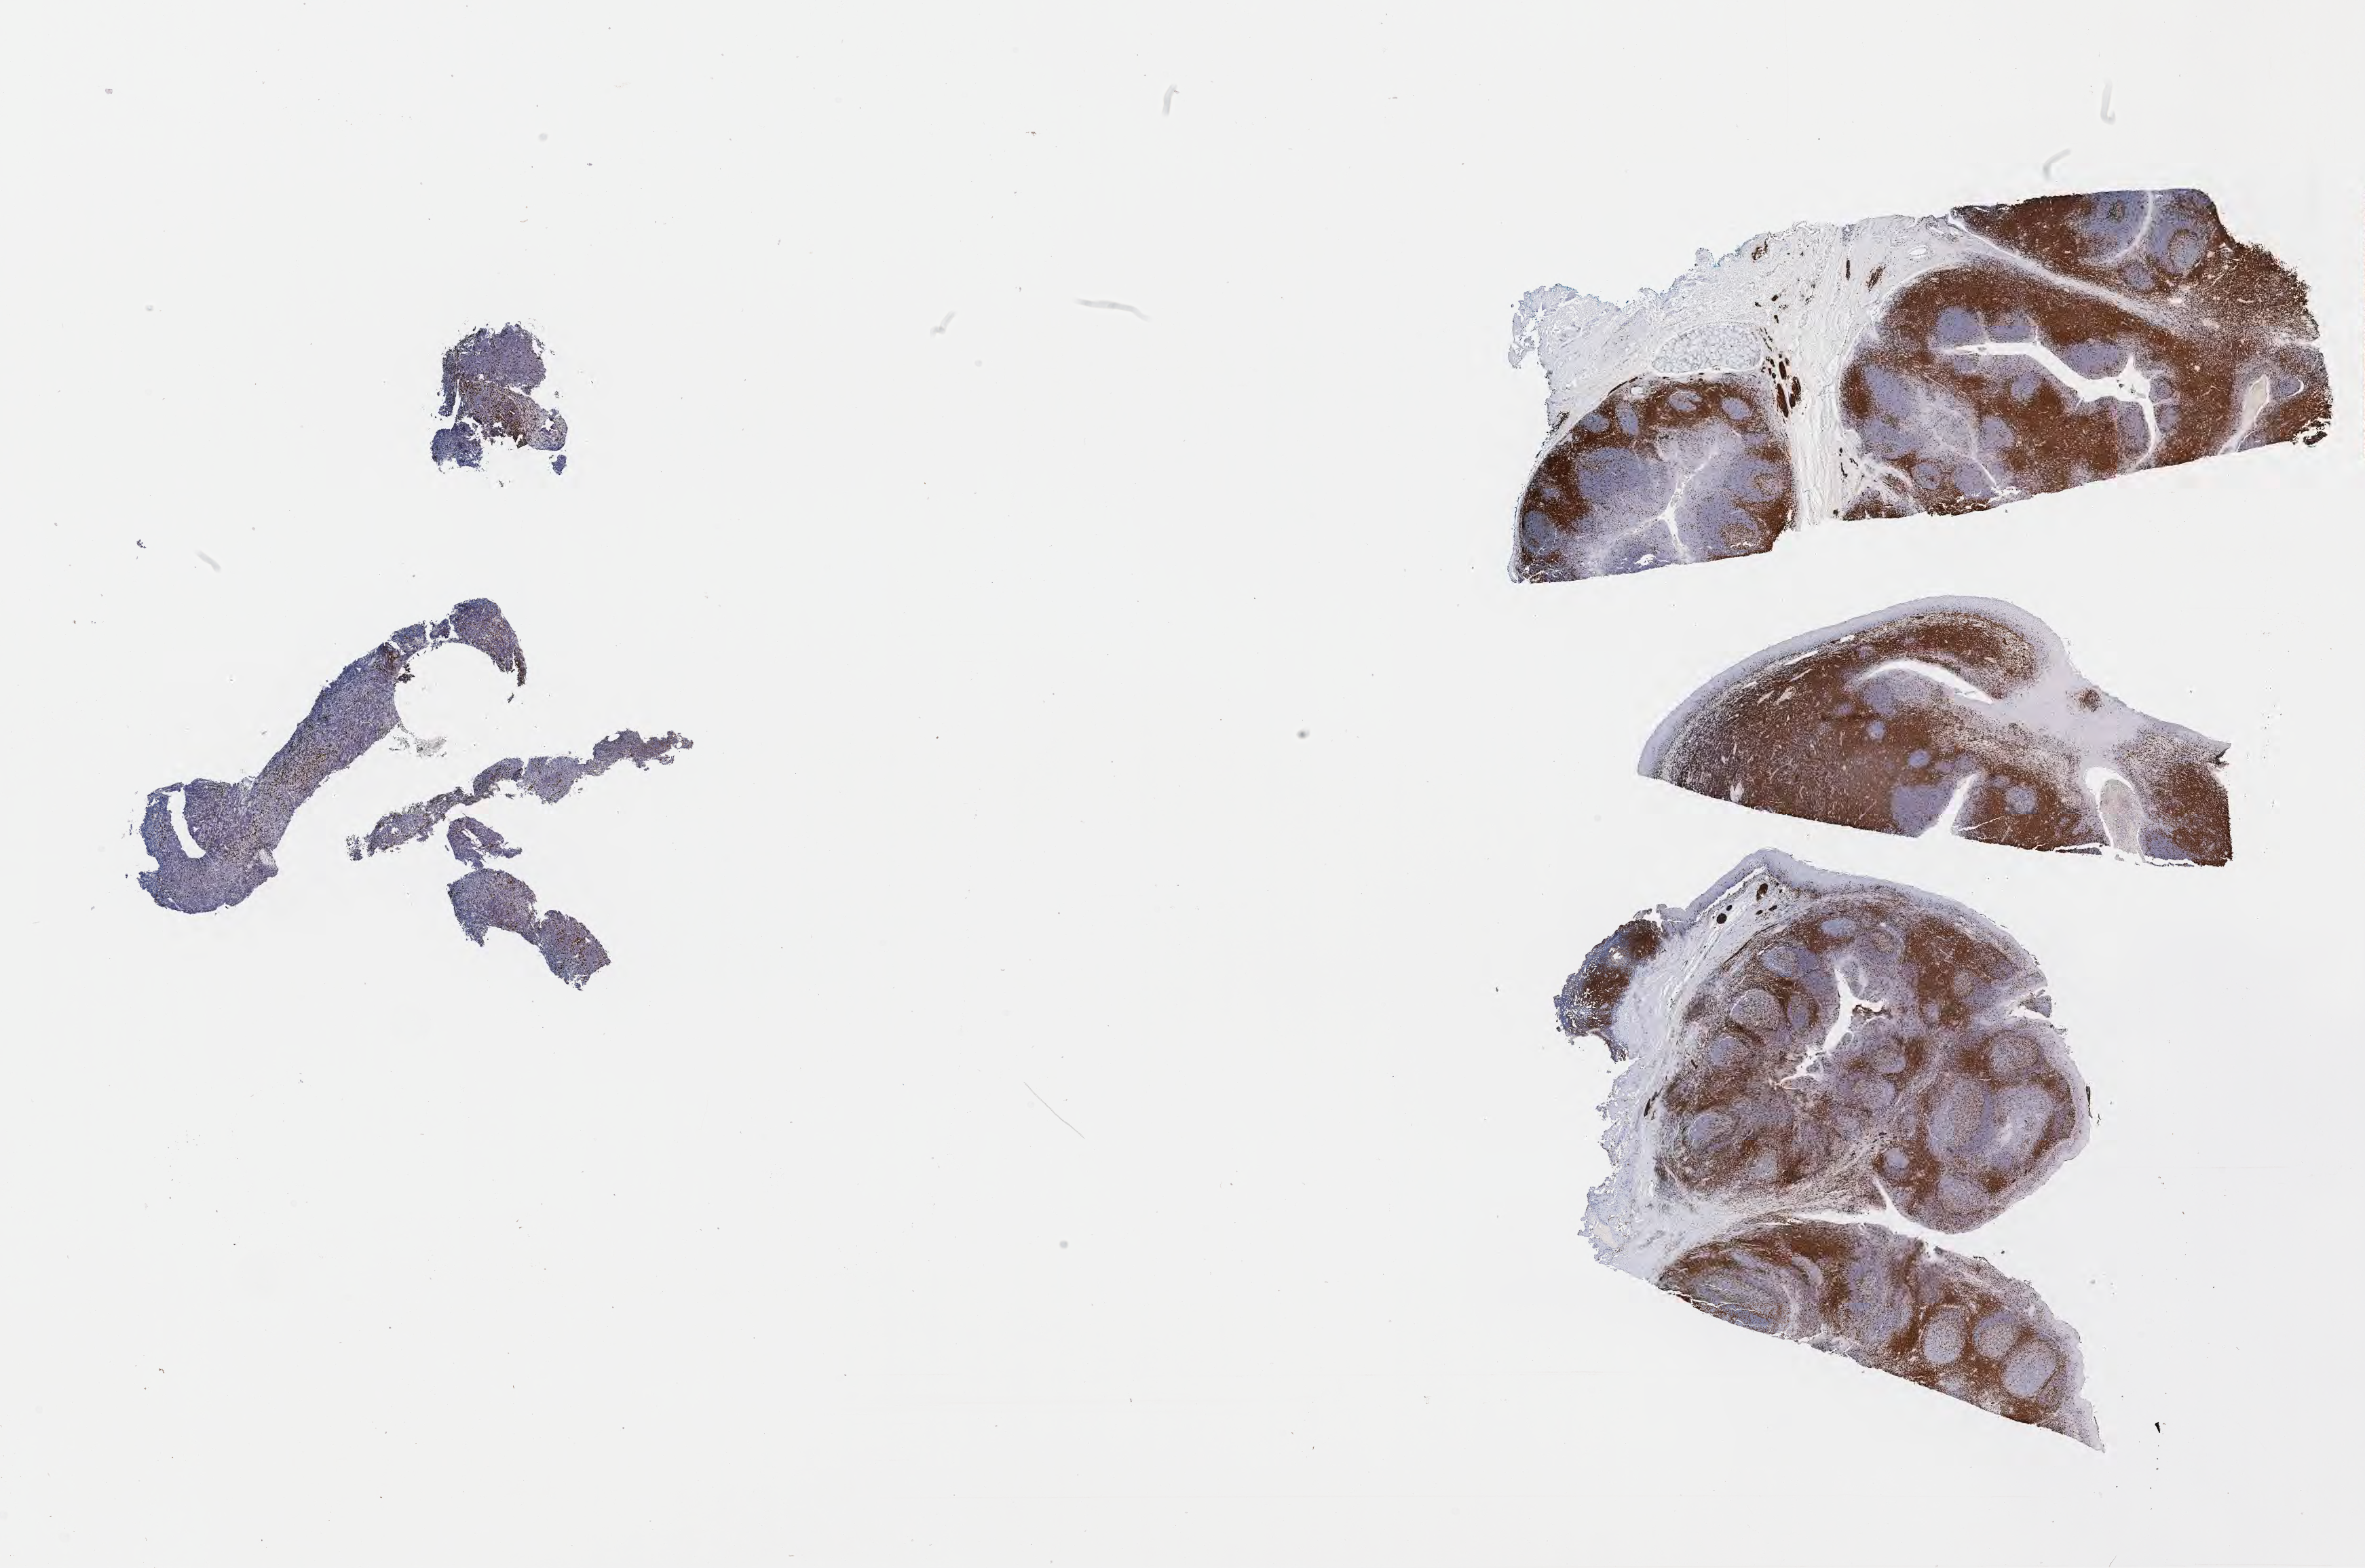
Whole-slide image, immunohistochemical stain for CD3, low-resolution overview of the scanned area, about 28.2 x 18.7 mm; specimen: tumor tissue; anatomic site: cranium. Patient: male, age at initial diagnosis 5 years.
Histologic diagnosis: Burkitt lymphoma, NOS.